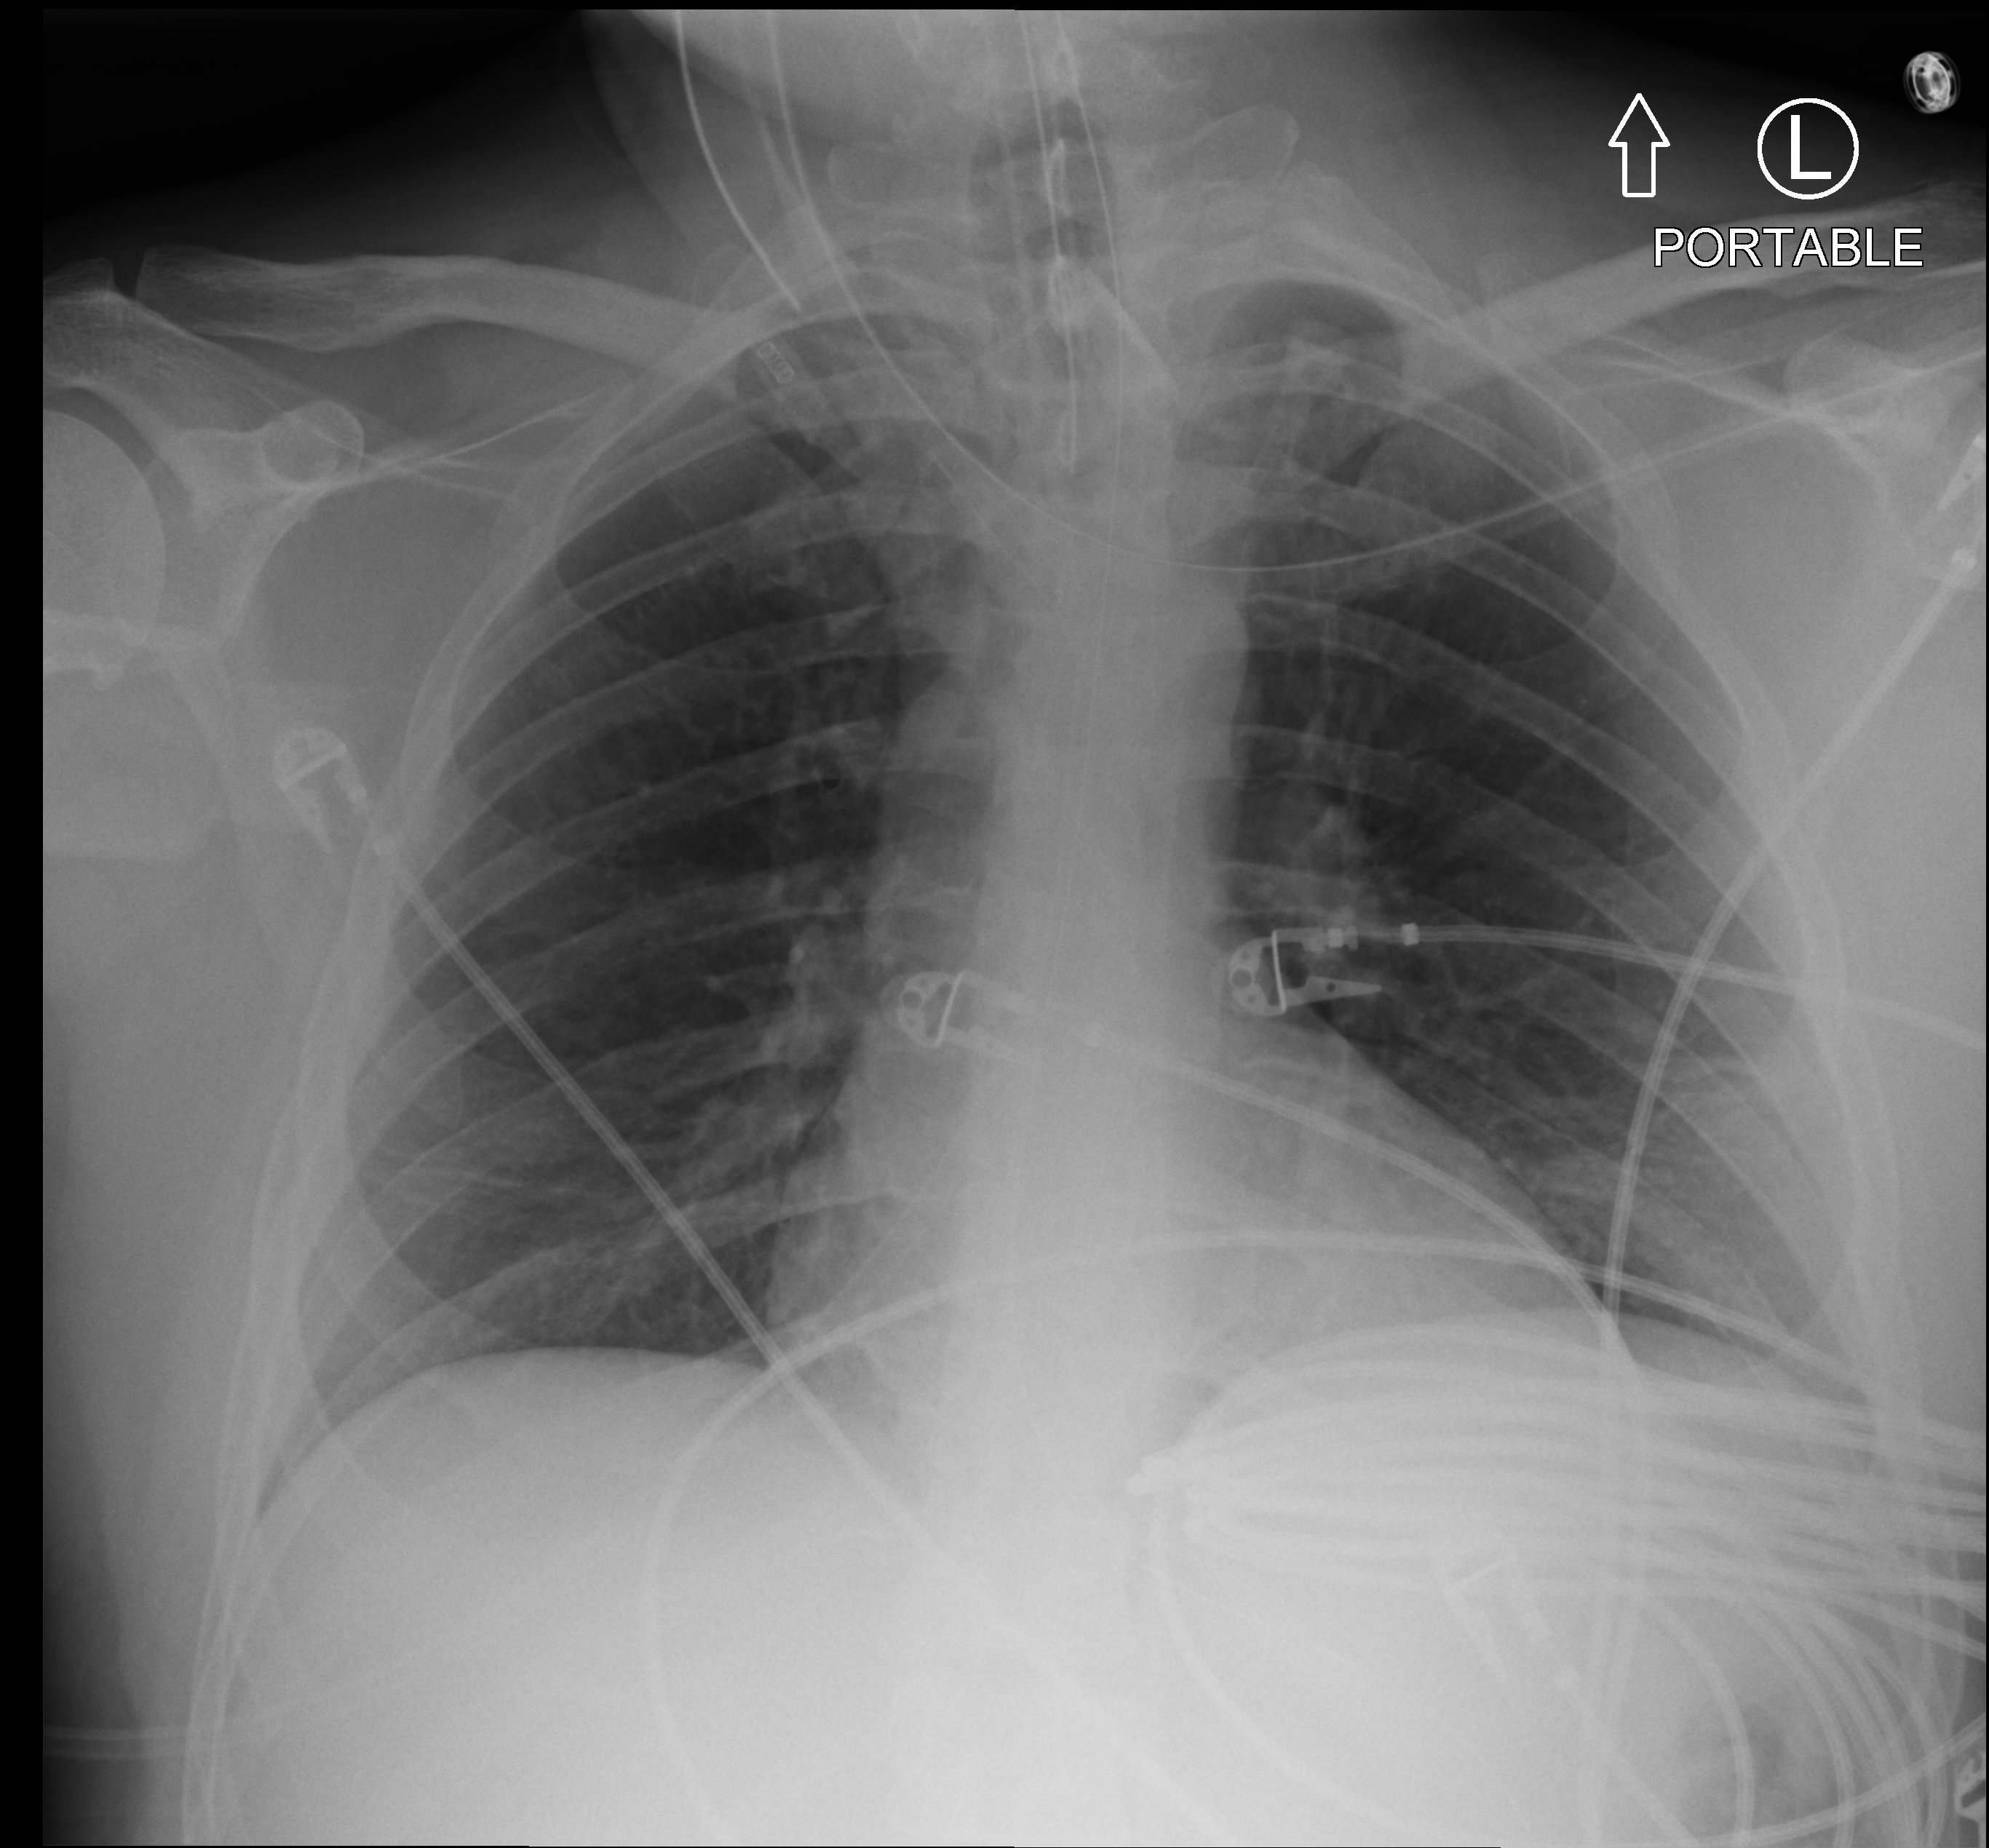
Chest X-ray (portable); anteroposterior (AP) projection. Male patient hospitalised with COVID-19, age 18–59 years.
Hospital-stay facts (about this admission, not read from this image; timing relative to this image not recorded): mechanically ventilated during this hospital stay: yes.